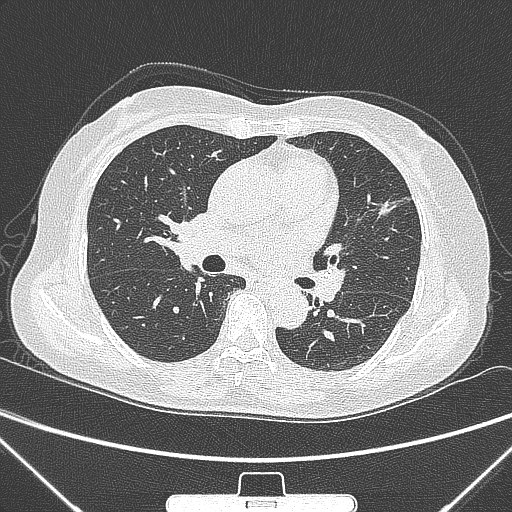
Chest CT, one axial slice; position 152 of 300 along the scan axis; lung window (W 1500 / L -600 HU); 1 mm slice thickness; 512 × 512 image matrix, field of view 350 × 350 mm. Patient: female, 70 years. From the clinical record (not read from this slice): clinical TNM (as recorded): T1b N0 M0; histopathological grade: G2.
Annotated regions visible in this slice (bounding box drawn by a radiologist):
- lung tumour (recorded histology: adenocarcinoma): bounding box (x1, y1, x2, y2) in pixels: (369, 192, 398, 228)